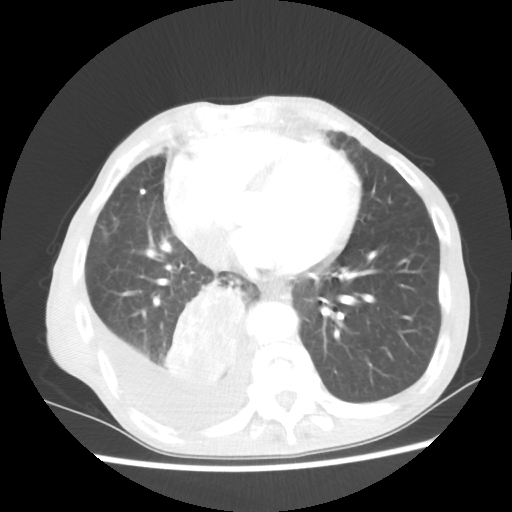
Chest CT, one axial slice. Slice 22 of 60 in the series (ordered by position). Reconstruction kernel STANDARD. Lung window (W 1500 / L -600 HU). 5 mm slice thickness. 512 × 512 image matrix, field of view 335 × 335 mm. Male patient, age 76 years. Case-level facts recorded for this patient, not image findings: clinical TNM (as recorded): T3 N3 M1a; histopathological grade: G3.
Outlined on this slice (bounding box drawn by a radiologist):
- lung tumour (recorded histology: squamous cell carcinoma): bounding box [x1, y1, x2, y2] px = [161, 278, 247, 386]